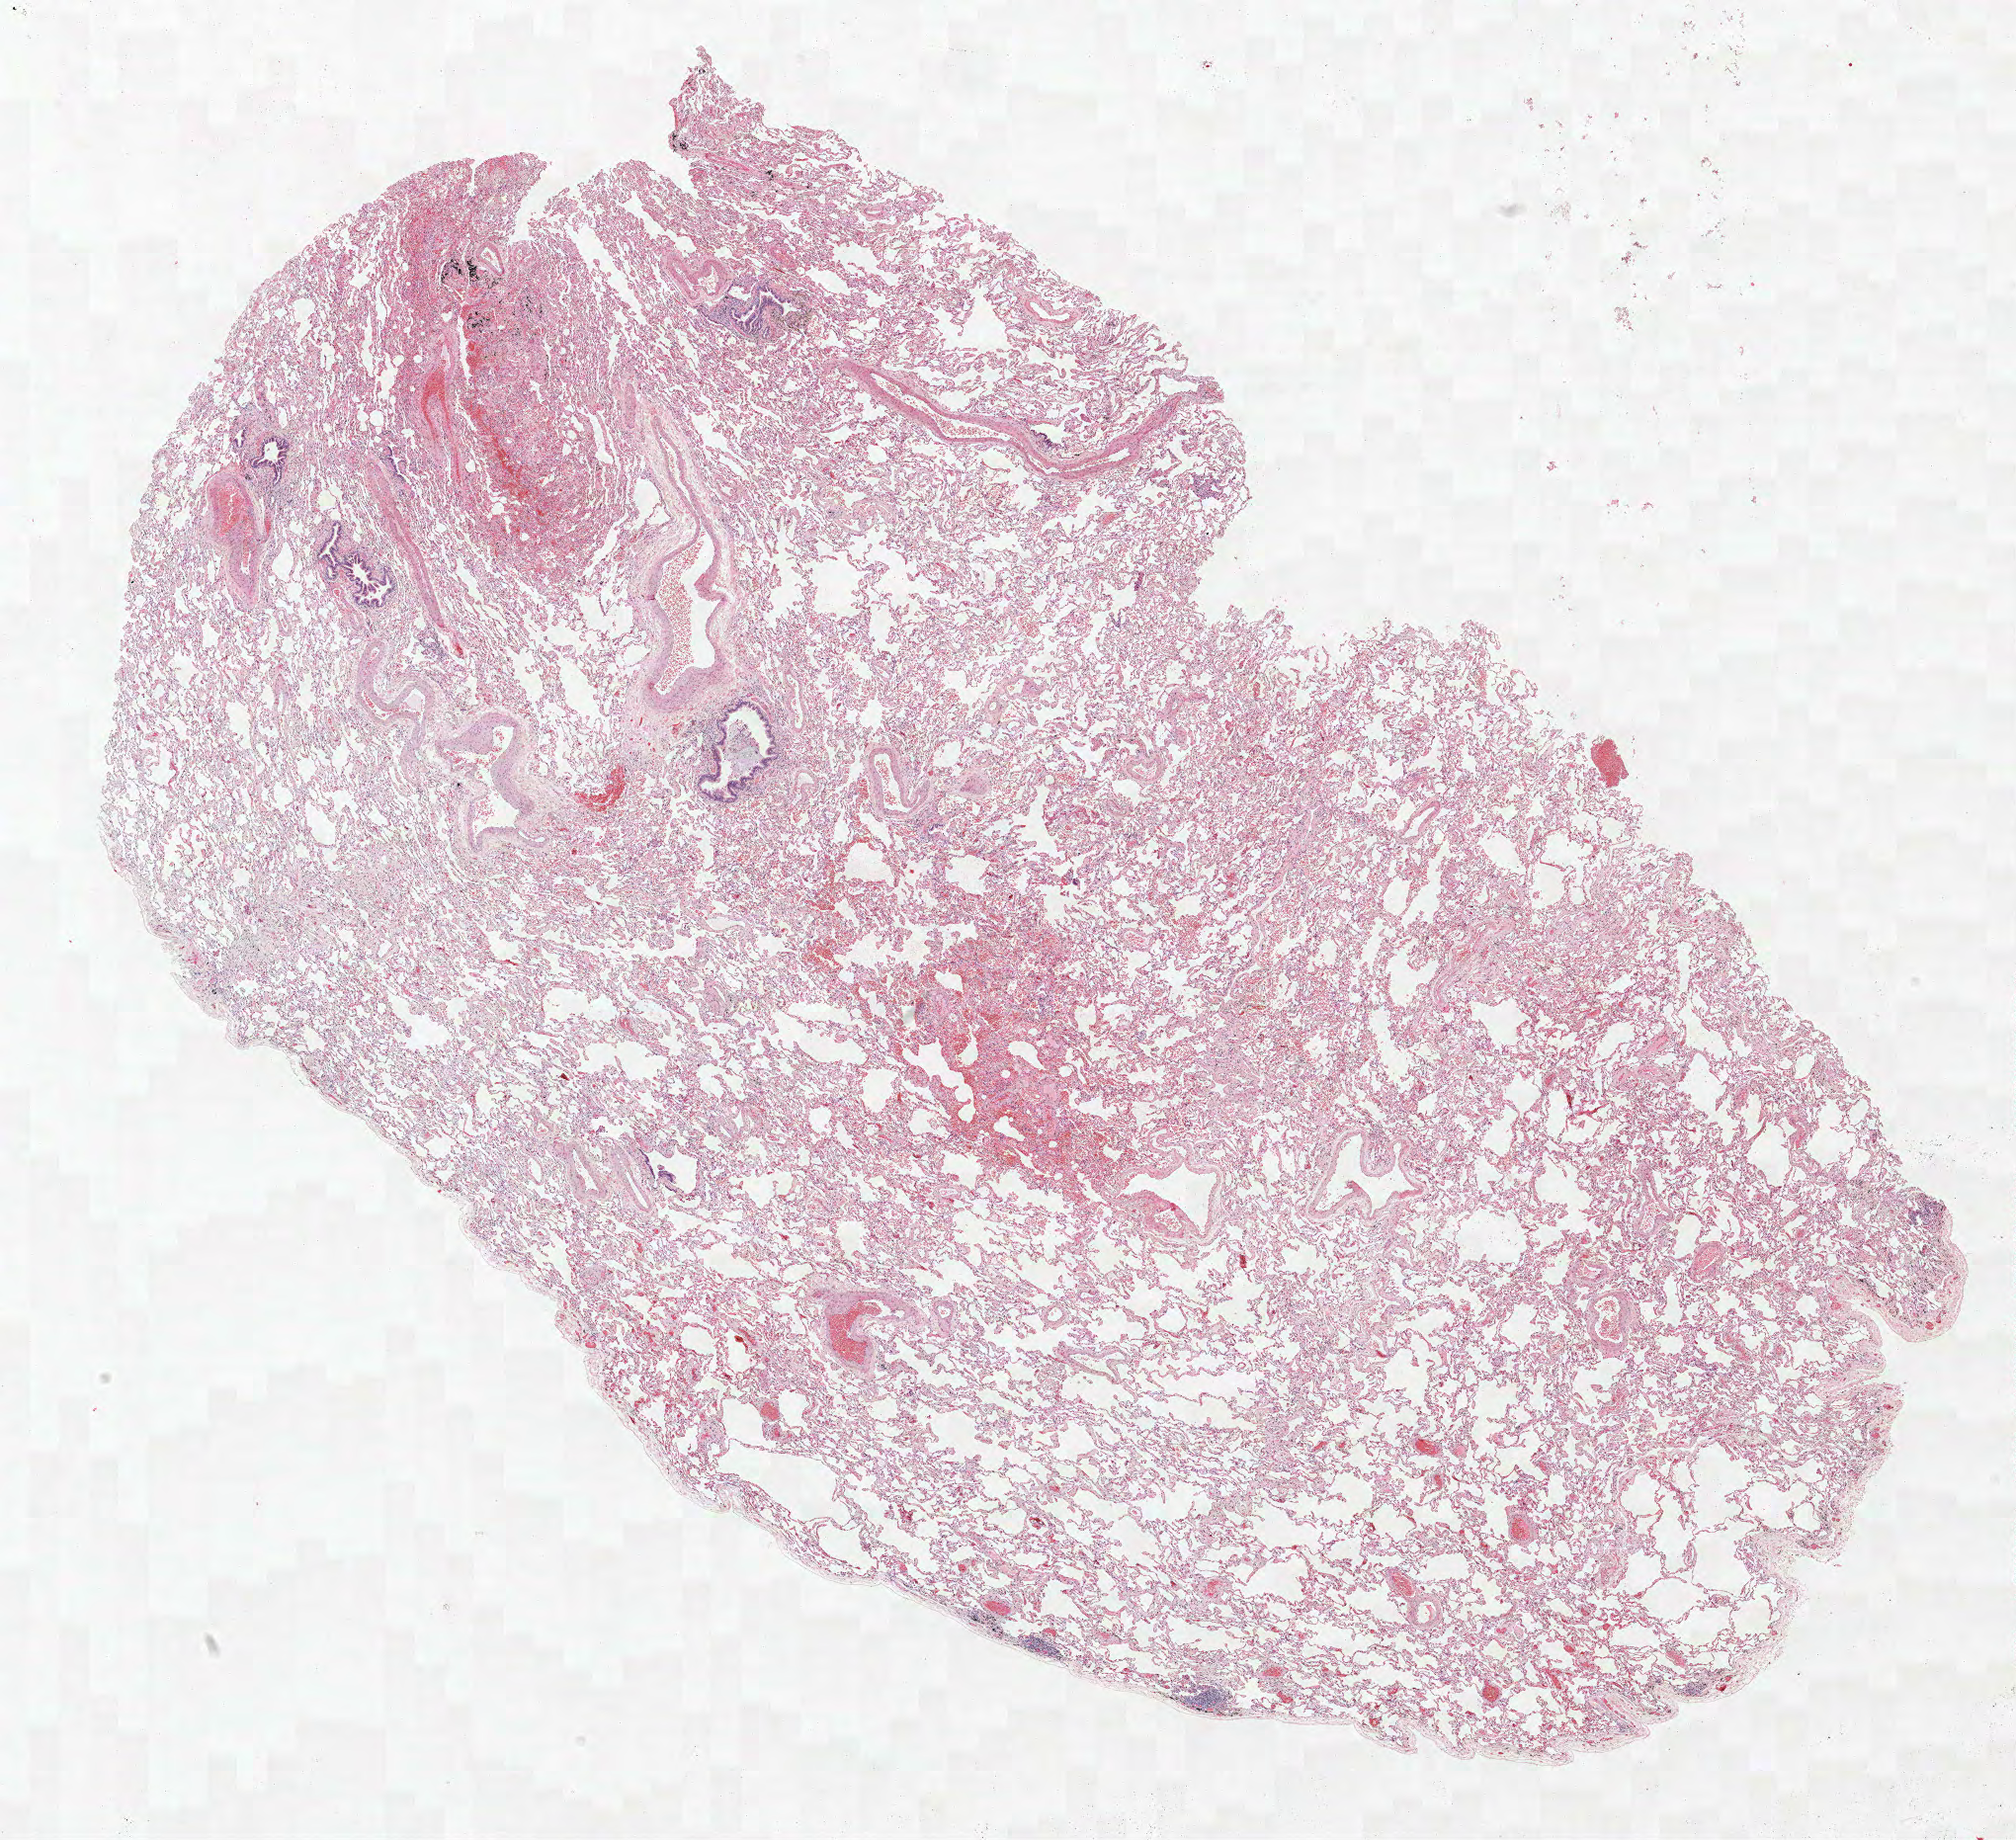
H&E whole-slide image — whole scanned area (about 16.3 x 14.9 mm, acquisition: 40x scan) shown as a low-resolution overview; formalin-fixed paraffin-embedded (FFPE) section; lung tissue. Female, age 55 at enrolment. Grade: well differentiated (G1).
Participant's lung-cancer diagnosis: Bronchiolo-alveolar adenocarcinoma, NOS (ICD-O-3 8250/3). Tumour size (pathology): 12 mm. Stage (AJCC 6th edition): IA. Primary tumour location (clinical record): right lower lobe.